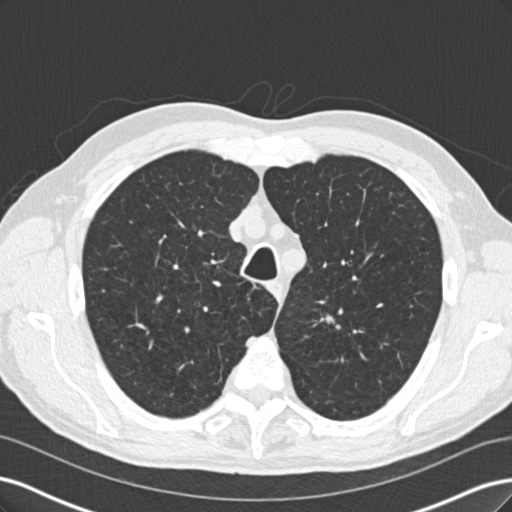
Low-dose screening chest CT, one axial slice. Position 174 of 219 along the scan axis. Lung window (W 1500 / L -600 HU). 2 mm slice thickness. 512 × 512 image matrix, field of view 360 × 360 mm.
Outlined on this slice (outlined manually by an expert reader):
- lesion 1 (tumor, upper lobe of left lung): box from (x=324, y=308) to (x=343, y=330) px